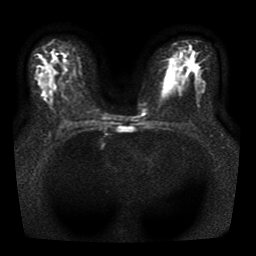
Breast MRI, one axial slice. Slice 25 of 41 in the series (ordered by position). Diffusion-weighted series; image 2 of 4 stored at this slice position (different b-values; order by instance number). 1.5 T. 5 mm slice thickness. 256 × 256 image matrix, field of view 330 × 330 mm. Female patient.
Annotated regions visible in this slice (manually delineated by an expert):
- tumour on diffusion-weighted imaging: bounding box (x1, y1, x2, y2) in pixels: (43, 90, 49, 97)